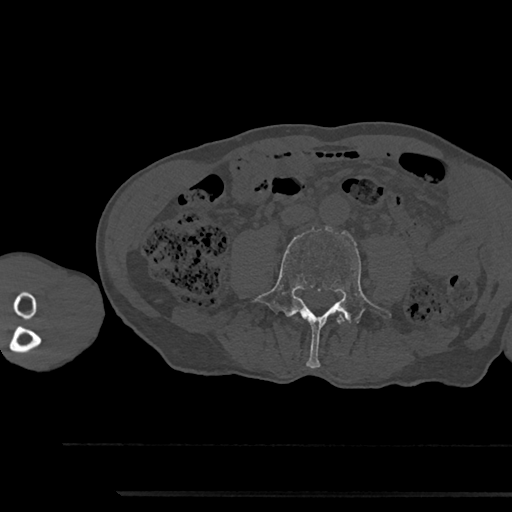
CT including the spine, one axial slice. Slice 423 of 797 in the series (ordered by position). Reconstruction kernel Br40s/3. 120 kVp. Bone window (W 1800 / L 400 HU). 0.5 mm slice thickness. 512 × 512 image matrix, field of view 367 × 367 mm. Patient: male, 79 years. Case-level facts recorded for this patient, not image findings: primary cancer: prostate.
Annotated regions visible in this slice (semi-automatic segmentation, software-assisted and operator-edited):
- L3 vertebra: box from (x=337, y=317) to (x=342, y=323) px
- L4 vertebra: (x=251, y=227)–(x=392, y=368)